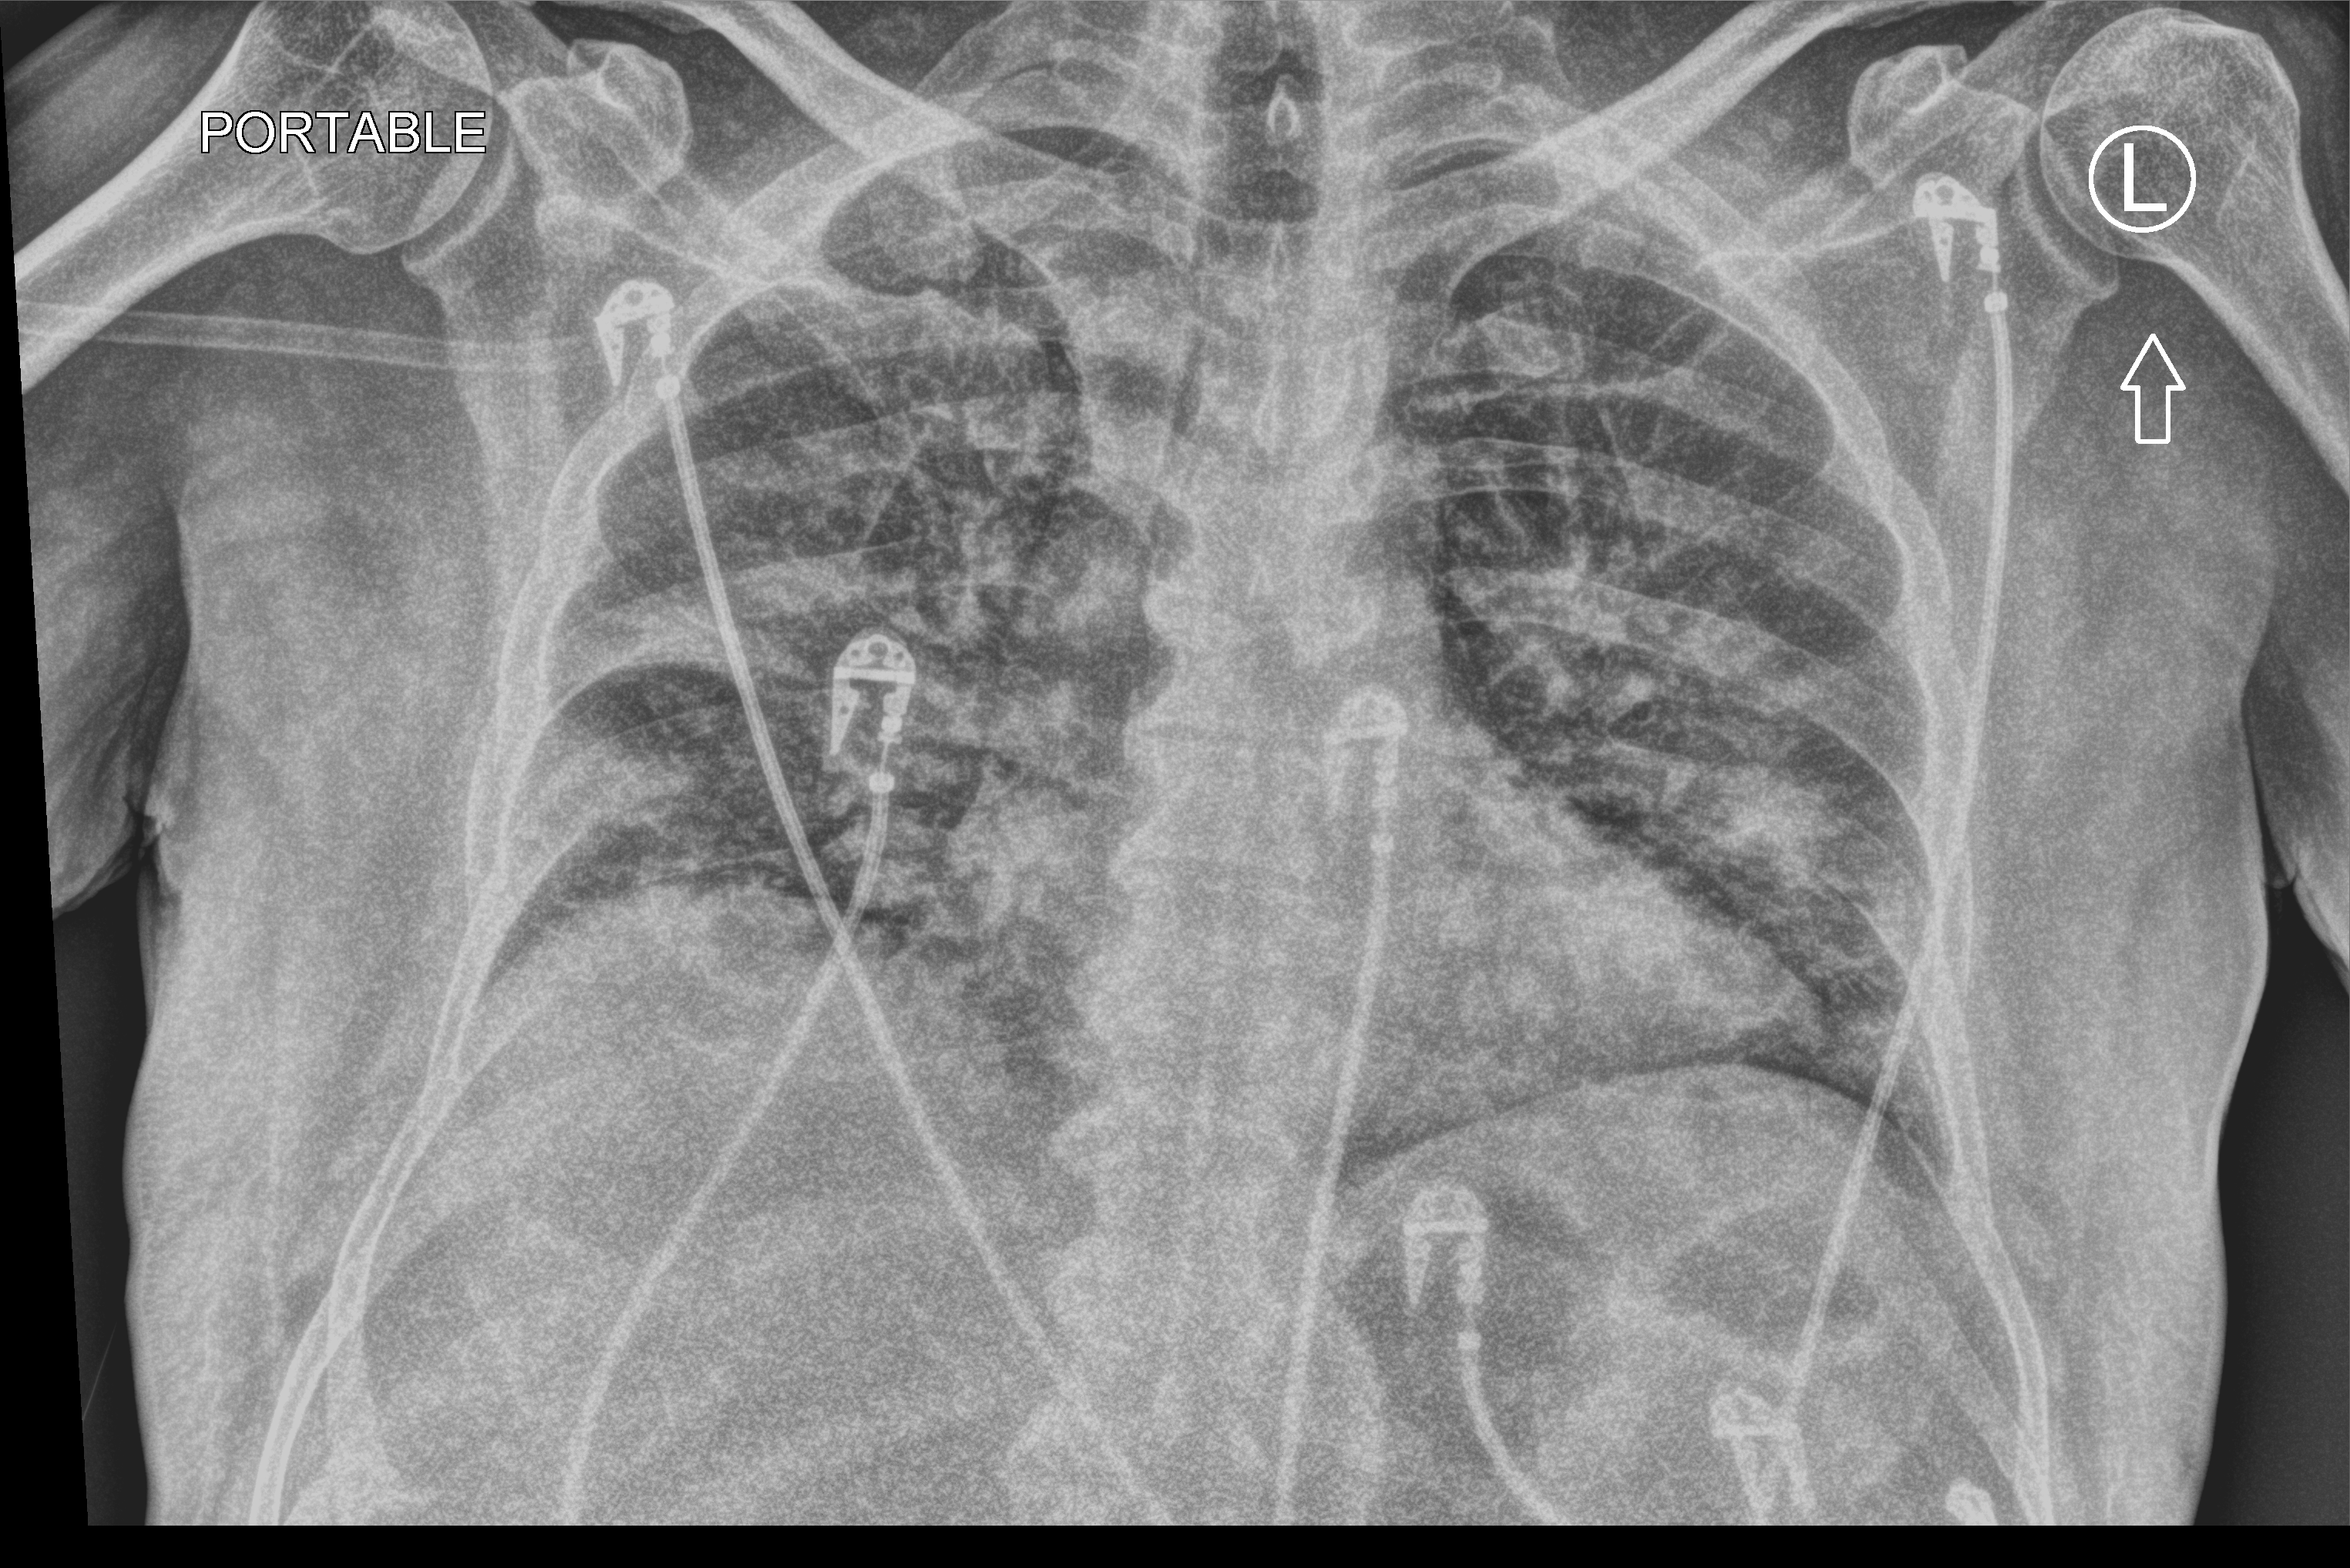
Portable chest radiograph, anteroposterior (AP) projection. Patient hospitalised with COVID-19; male, aged 60–74 years.
From the hospital-stay record, not from the radiograph (when in the stay this image was taken is not recorded): admitted to intensive care during this hospital stay: yes.